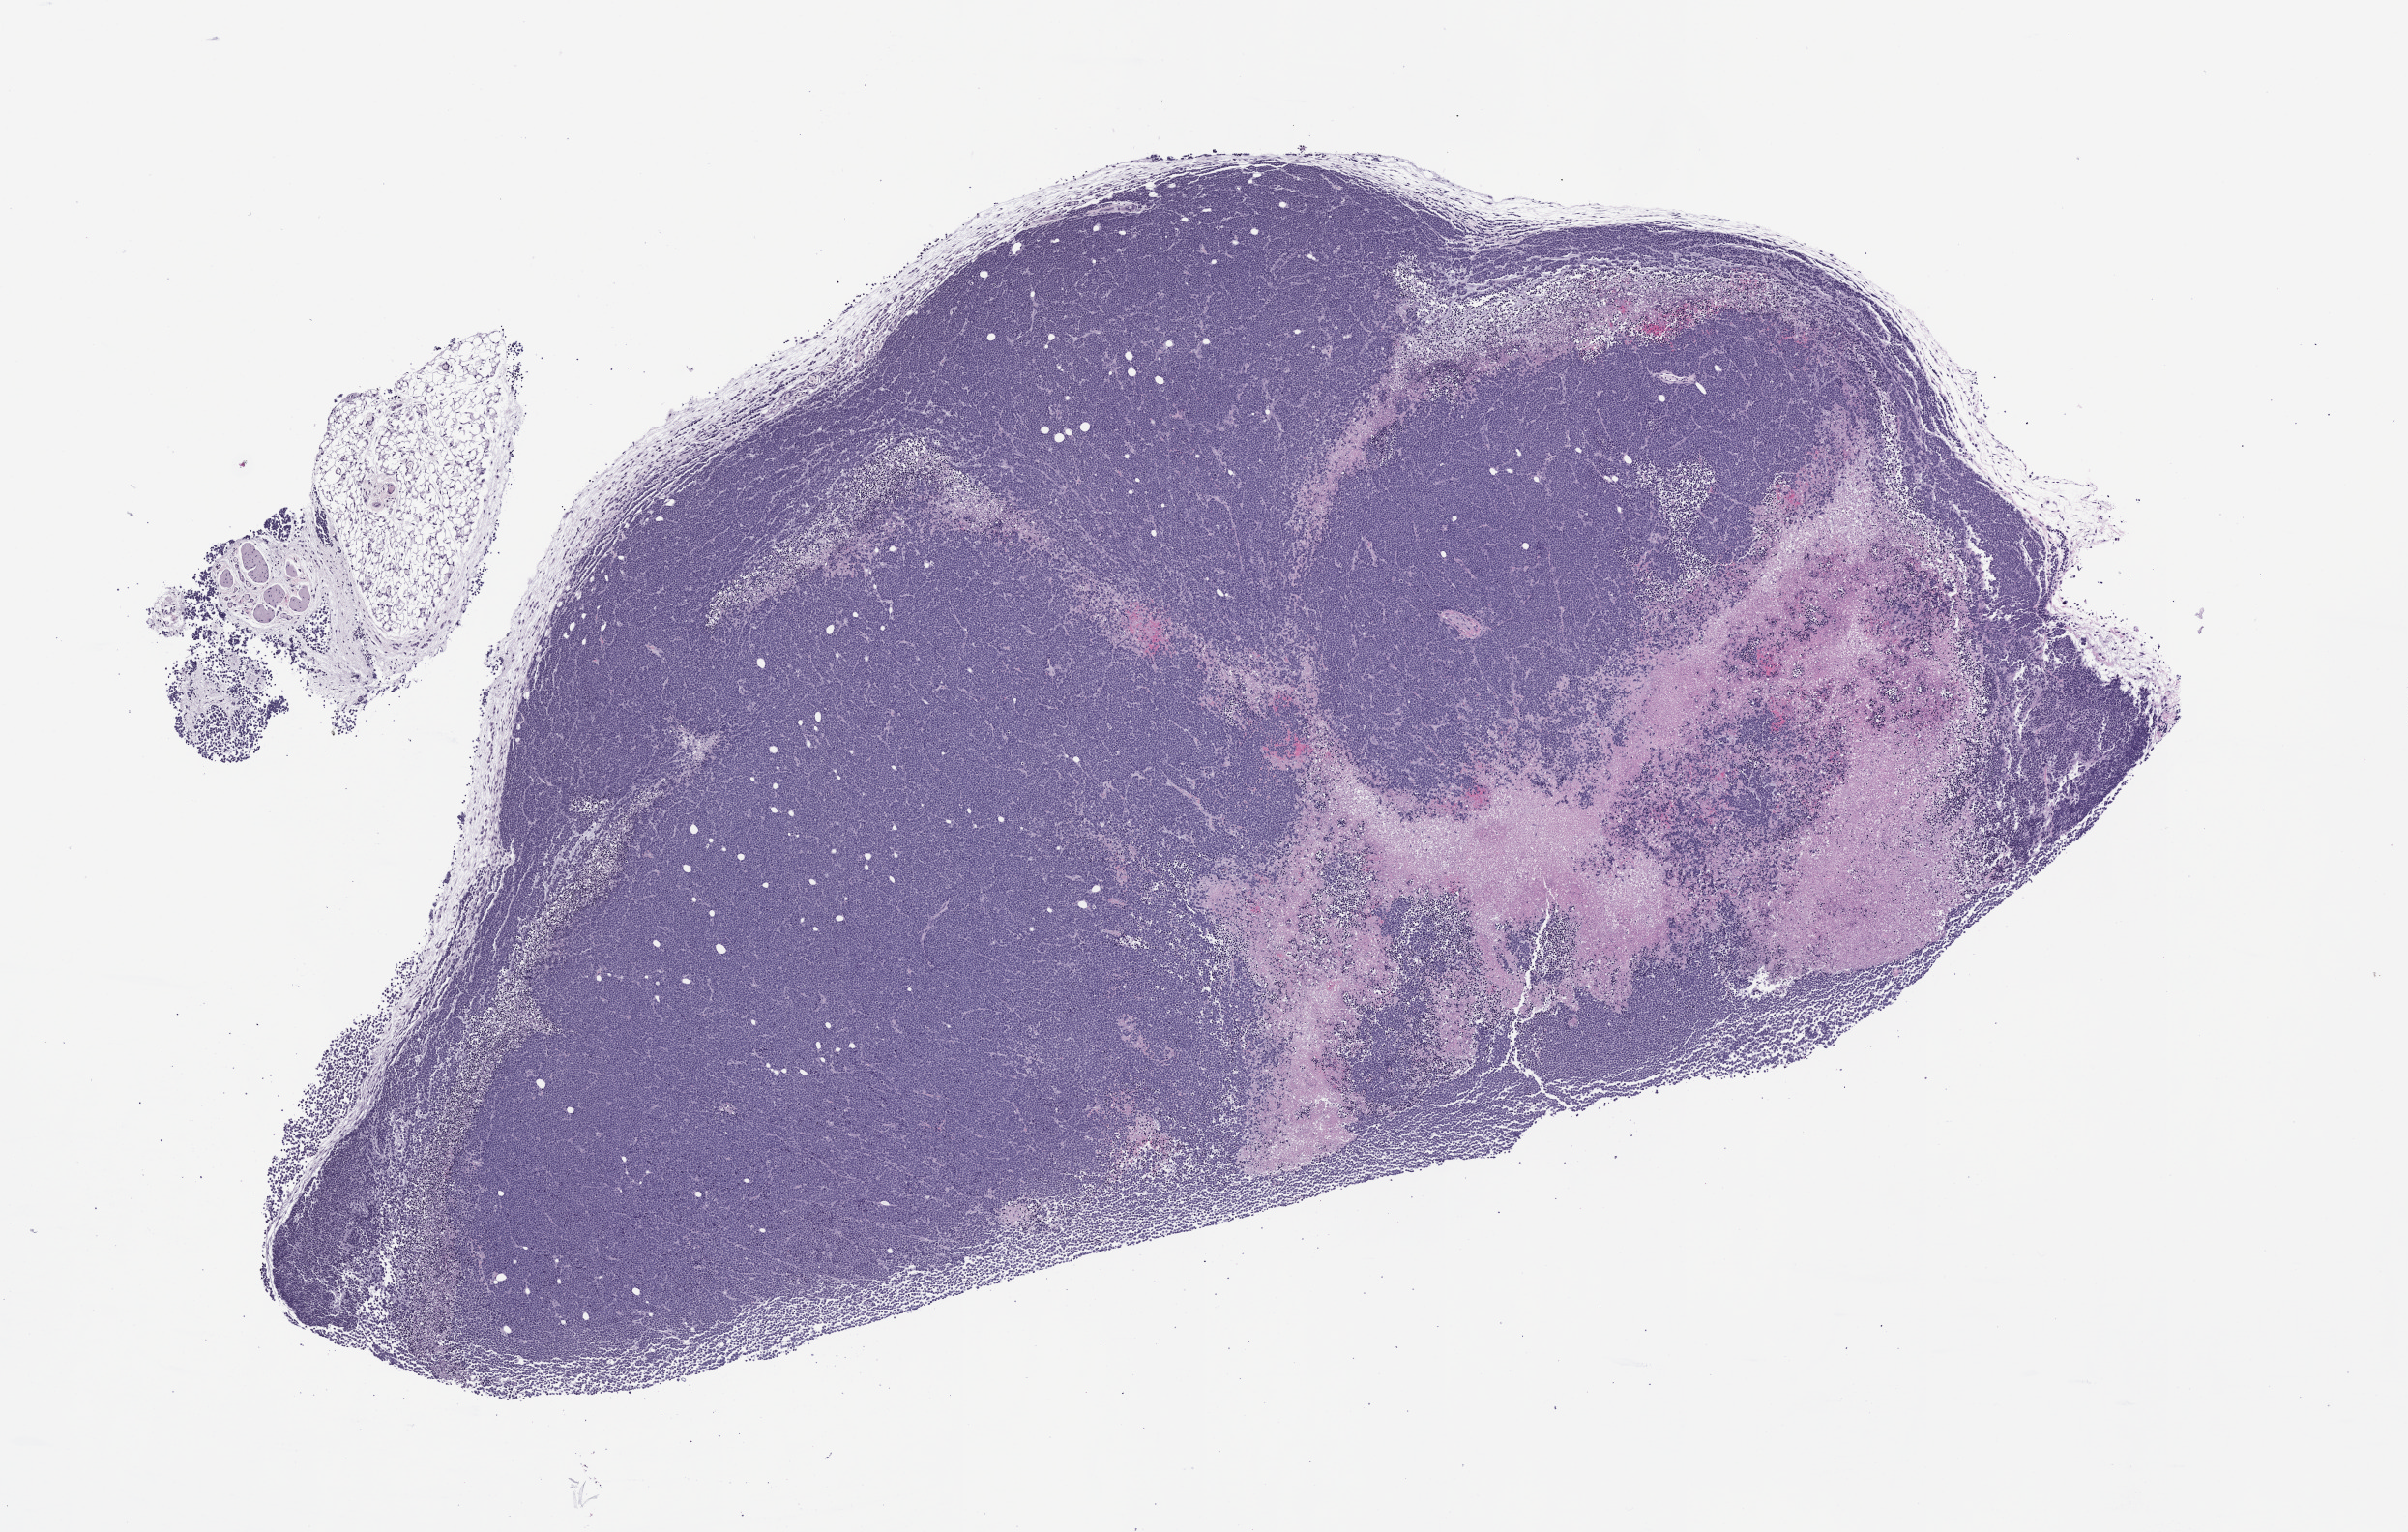
H&E whole-slide image of a patient-derived xenograft (PDX) tumor grown in a mouse, passage 1 — shown as a low-resolution overview of the whole scanned area (about 10.0 x 6.4 mm). Formalin-fixed paraffin-embedded section. Tumor site category: lung.
Originating patient diagnosis: Lung Small Cell Carcinoma.